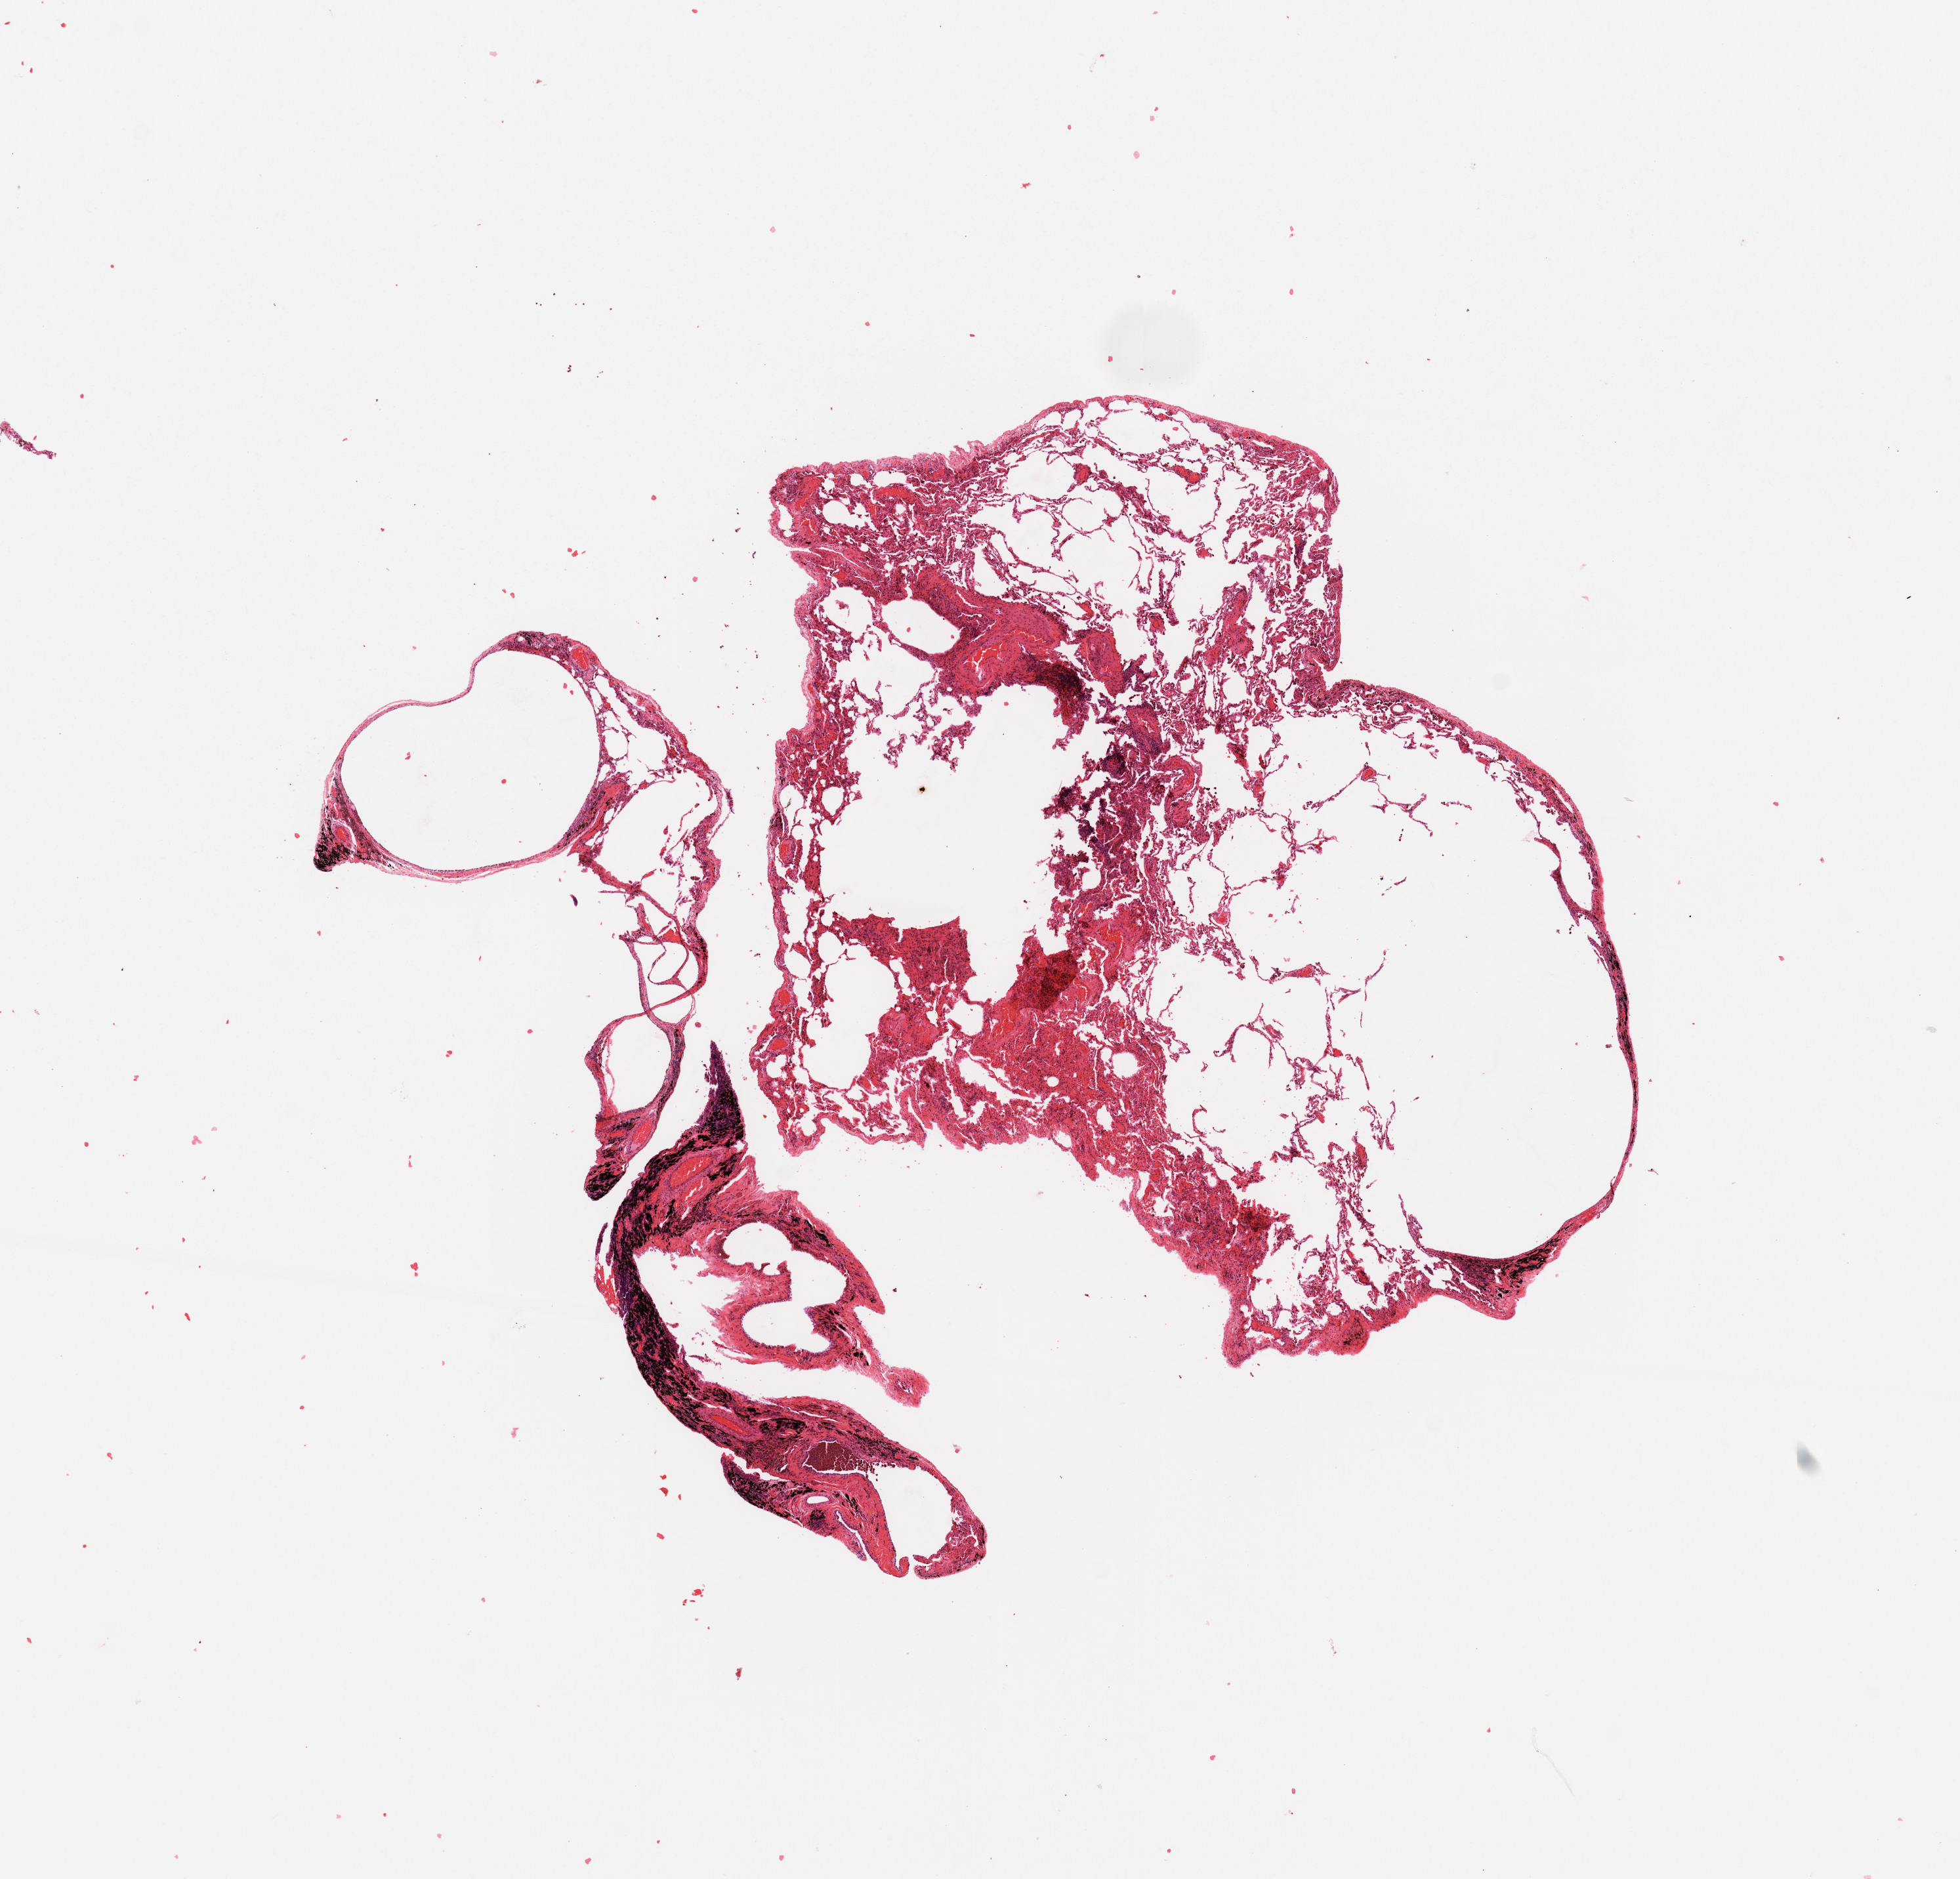
Hematoxylin and eosin (H&E) stained whole-slide image — shown as a low-resolution overview of the whole scanned area (about 11.8 x 11.3 mm), normal (non-tumour) tissue sample, sampled site: lung. 62-year-old male patient.
This section: normal (non-tumour) tissue from the same patient. Patient diagnosis: Squamous cell carcinoma, NOS.